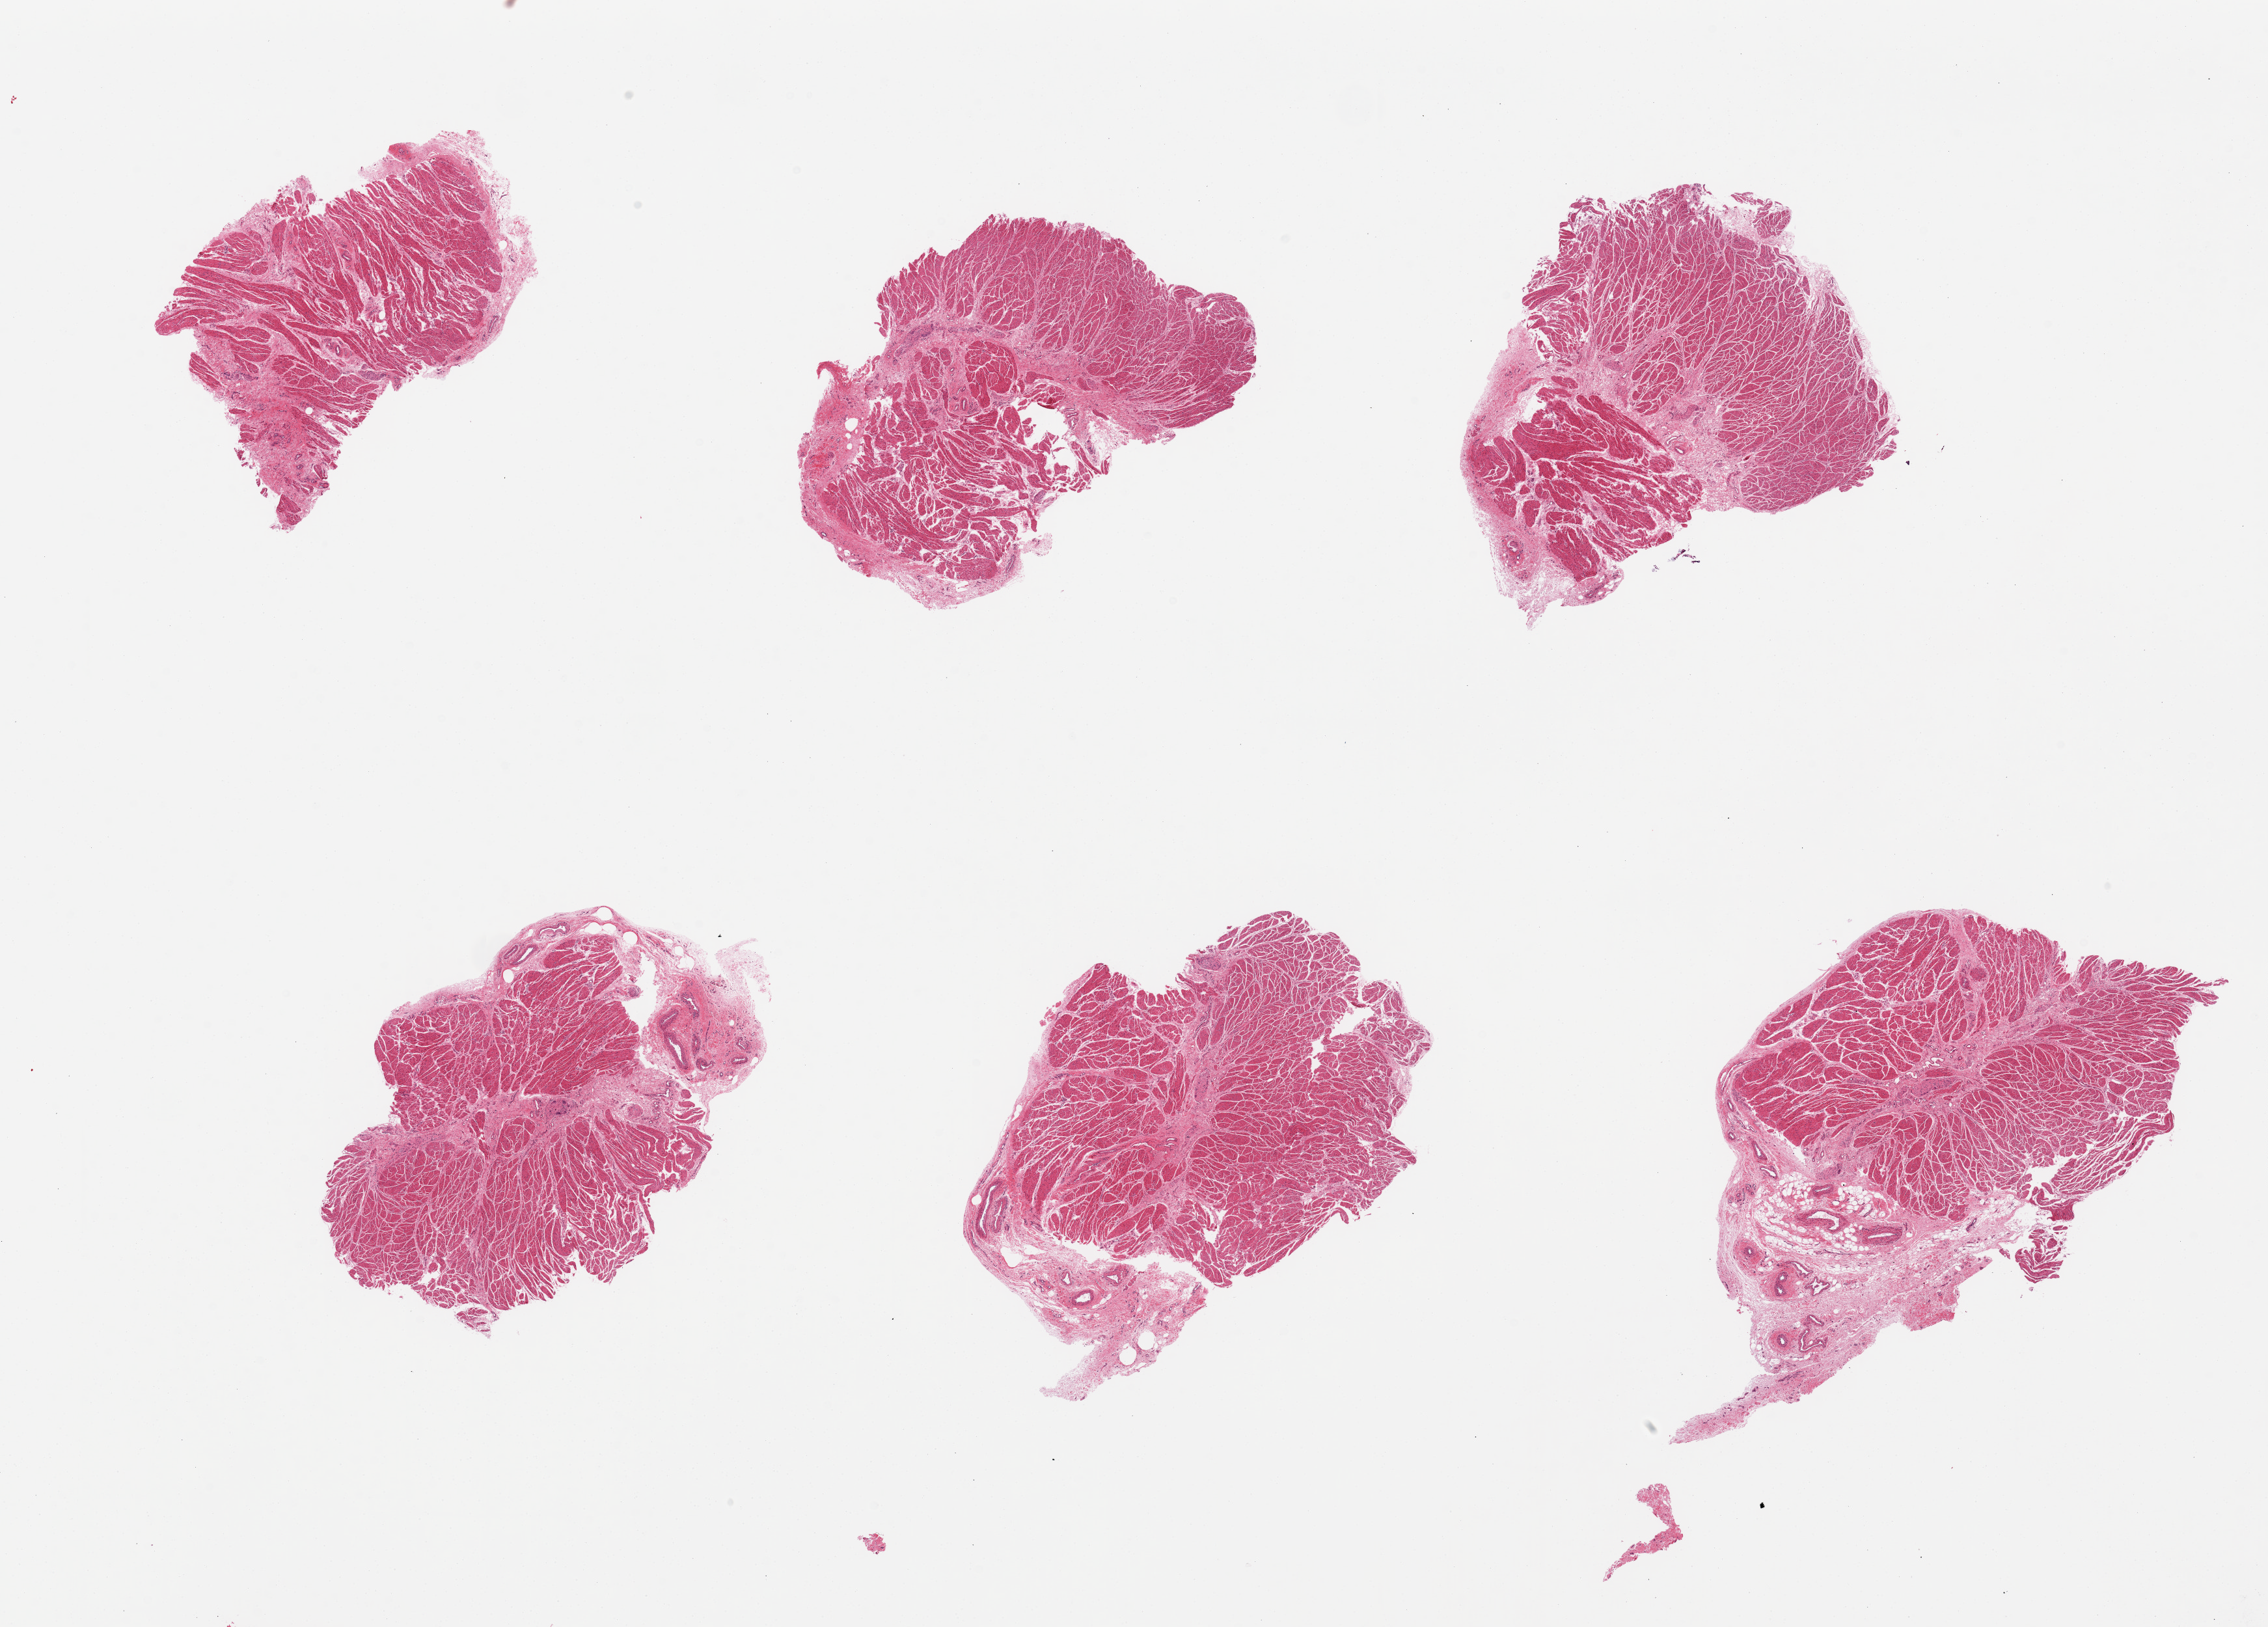
Whole-slide image, hematoxylin and eosin (H&E) stain, brightfield — low-resolution overview of the scanned area, about 27.6 x 19.8 mm. PAXgene-fixed, paraffin-embedded tissue. Section of gastroesophageal junction (target tissue). Donor tissue sample. Donor sex: male.
• pathologist's review note for this sample: 6 pieces; all muscularis